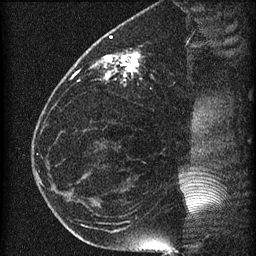
Breast MRI (dynamic contrast-enhanced), one sagittal slice. Slice 24 of 60 in the series (ordered by position). Dynamic contrast-enhanced series, image 2 of 4 at this slice position (ordered by acquisition). 1.5 T. TE 4.2 ms, TR 22.7 ms. 1.5 mm slice thickness. 256 × 256 image matrix, field of view 180 × 180 mm. Patient: female, 35 years. Case-level facts recorded for this patient, not image findings: setting: breast cancer imaged before/during neoadjuvant chemotherapy; receptor status: HR-positive, HER2-negative.
Outlined on this slice (semi-automatic segmentation, software-assisted and operator-edited):
- analysis volume of interest (the breast-tissue region the enhancement analysis was run in; not a lesion): box from (x=69, y=27) to (x=199, y=112) px
- tumour enhancement mask (voxels above the 90 % enhancement threshold inside the analysis volume of interest): (x=73, y=51)–(x=141, y=80)